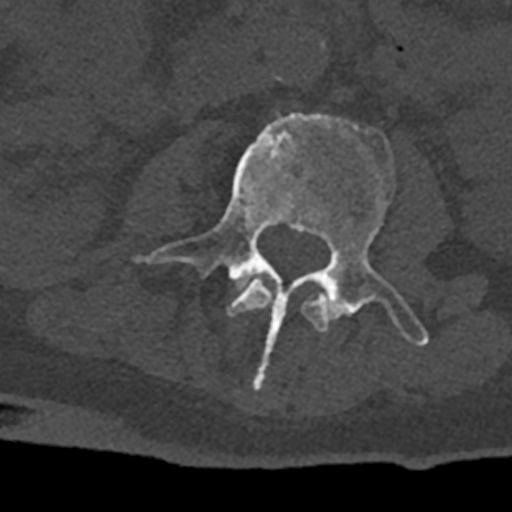
CT including the spine, one axial slice. Slice 329 of 797 in the series (ordered by position). Reconstruction kernel Br40s/3. 120 kVp. Bone window (W 1800 / L 400 HU). 0.5 mm slice thickness. 512 × 512 image matrix, field of view 160 × 160 mm. Patient: male, 74 years. From the clinical record (not read from this slice): primary cancer: renal; vertebrae with lytic lesions (as recorded): T10, L1, L2, L3, L4, L5.
Annotated regions visible in this slice (semi-automatic segmentation, software-assisted and operator-edited):
- L2 vertebra: bounding box <227,279,329,333> (left, top, right, bottom; pixels)
- L3 vertebra: <133,113,429,389>